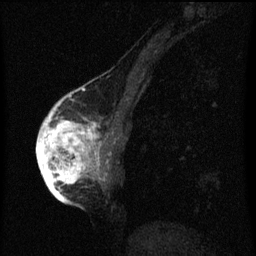
Breast MRI (dynamic contrast-enhanced), one sagittal slice. Slice 23 of 60 in the series (ordered by position). Dynamic contrast-enhanced series, image 2 of 3 at this slice position (ordered by acquisition). 1.5 T. TE 4.2 ms, TR 8 ms. 2 mm slice thickness. 256 × 256 image matrix, field of view 180 × 180 mm. Patient: female, 56 years.
Outlined on this slice (semi-automatic segmentation, software-assisted and operator-edited):
- analysis volume of interest (the breast-tissue region the enhancement analysis was run in; not a lesion): bounding box (x1, y1, x2, y2) in pixels: (42, 110, 103, 193)
- tumour enhancement mask (voxels above the 70 % enhancement threshold inside the analysis volume of interest): (42, 110, 101, 193)